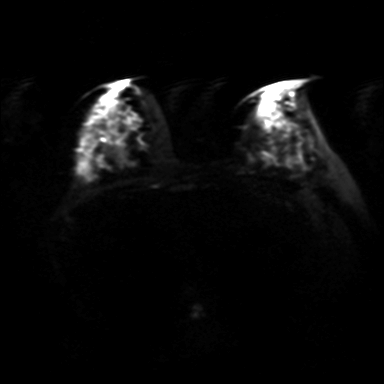
Breast MRI, one axial slice; slice 19 of 36 in the series (ordered by position); diffusion-weighted series; image 2 of 4 stored at this slice position (different b-values; order by instance number); 3 T; 4 mm slice thickness; 384 × 384 image matrix, field of view 320 × 320 mm. Female patient.
Structures marked on this image (outlined manually by an expert reader):
- tumour on diffusion-weighted imaging: bounding box (x1, y1, x2, y2) in pixels: (271, 104, 285, 119)